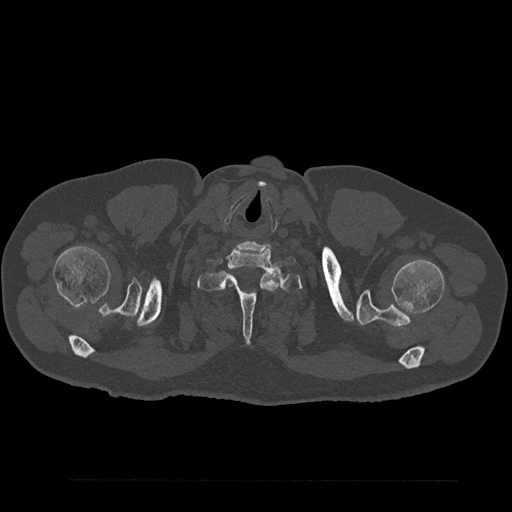
CT including the spine, one axial slice. Position 766 of 797 along the scan axis. 120 kVp. Bone window (W 1800 / L 400 HU). 0.5 mm slice thickness. 512 × 512 image matrix, field of view 430 × 430 mm. Patient: male, 61 years. Case-level facts recorded for this patient, not image findings: primary cancer: prostate.
Annotated regions visible in this slice (semi-automatically segmented with operator editing):
- T1 vertebra: bounding box (x1, y1, x2, y2) in pixels: (197, 261, 302, 339)